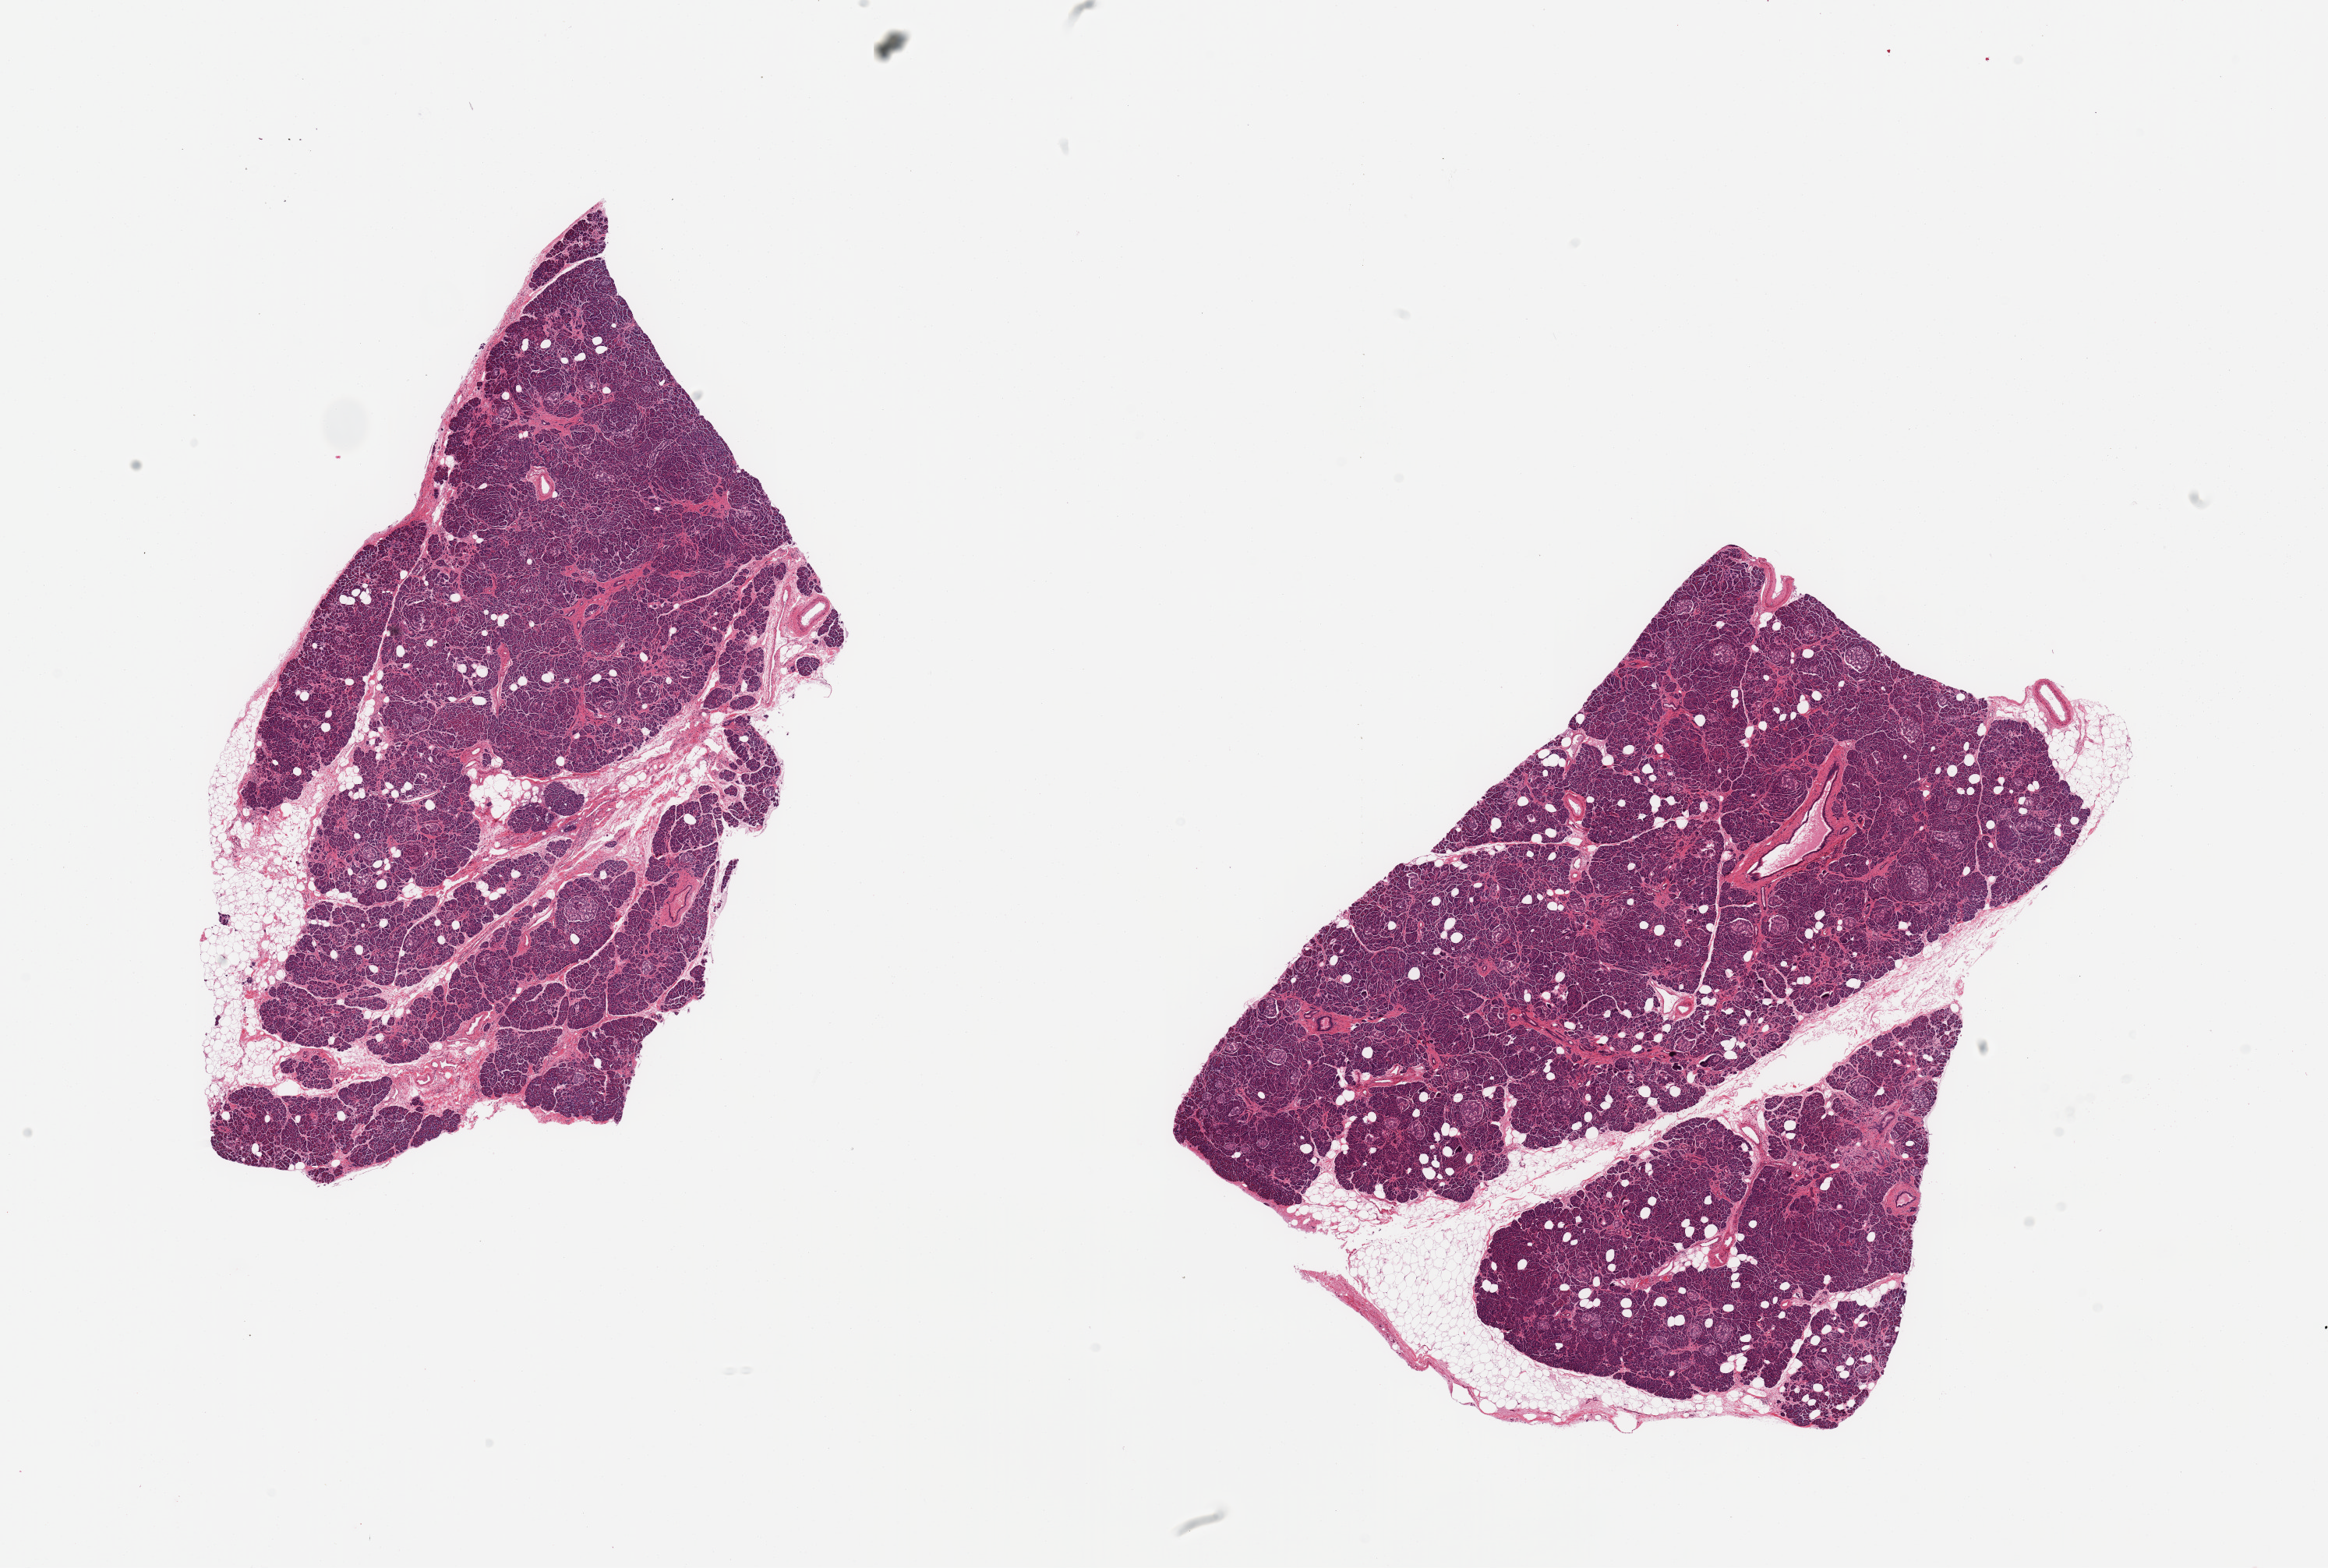
Digitized H&E-stained section — low-resolution overview of the scanned area, about 23.6 x 15.9 mm (from a 20x scan), PAXgene-fixed paraffin-embedded (PFPE) section, target tissue: pancreas, tissue donor sample. Donor sex: female.
Reviewer comment on this tissue sample: 2 pieces; focal periductal fibrosis; 10% external fat content; 5% internal fat.